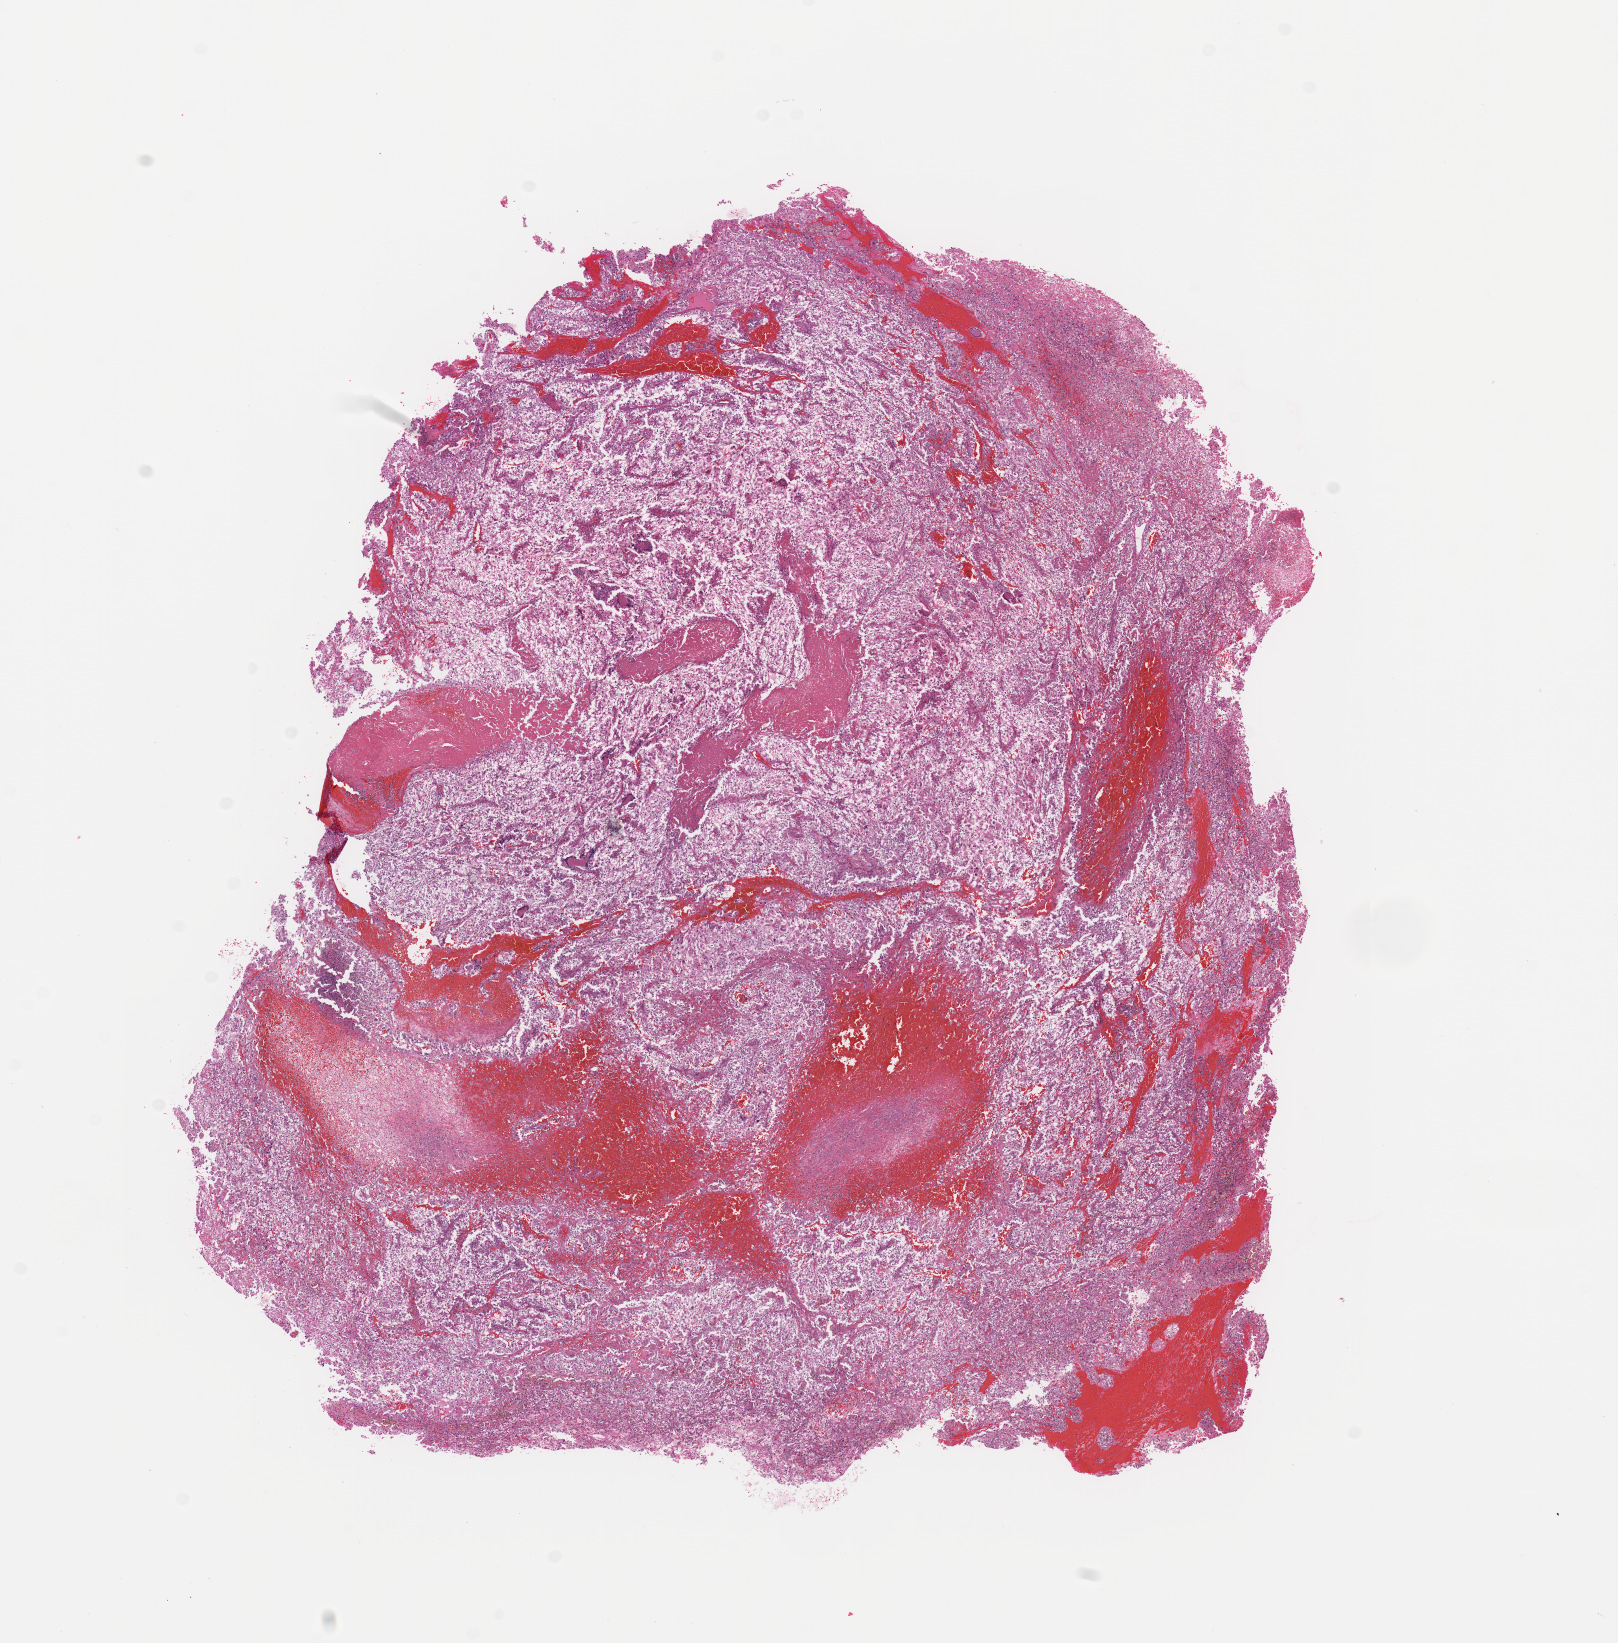
H&E whole-slide image — whole scanned area (about 12.8 x 13.0 mm, slide scanned at 20x) shown as a low-resolution overview. Kidney, tumour tissue. Patient: male, age 68 years. Histologic grade: G4 (undifferentiated).
AJCC pathologic stage: IV. Histologic diagnosis: Renal cell carcinoma, NOS.